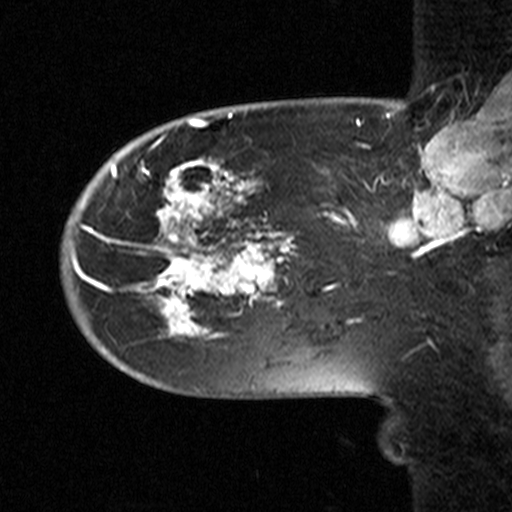
Breast MRI (dynamic contrast-enhanced), one sagittal slice. Slice 12 of 44 in the series (ordered by position). Dynamic contrast-enhanced study with each time point stored as its own series, time point 2 of 3 at this slice position (early post-contrast, ordered by acquisition time). 1.5 T. TE 4.5 ms, TR 11 ms. 3.27 mm slice thickness. 512 × 512 image matrix. Female patient, age 53 years. From the clinical record (not read from this slice): setting: breast cancer imaged before/during neoadjuvant chemotherapy; receptor status: HR-positive, HER2-negative.
Structures marked on this image (semi-automatic segmentation, software-assisted and operator-edited):
- analysis volume of interest (the breast-tissue region the enhancement analysis was run in; not a lesion): bounding box [x1, y1, x2, y2] px = [58, 154, 311, 367]
- tumour enhancement mask (voxels above the 90 % enhancement threshold inside the analysis volume of interest): [72, 160, 294, 338]